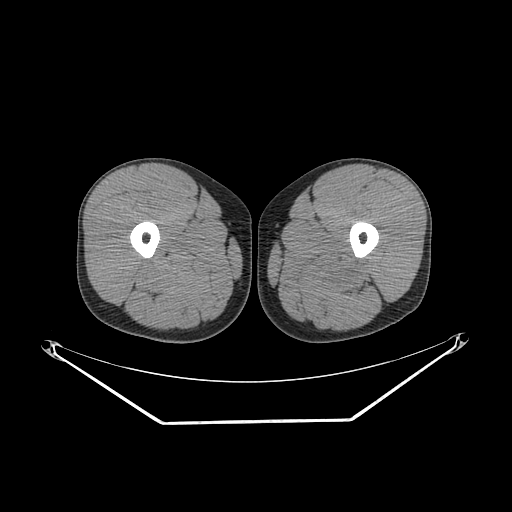
CT of an extremity soft-tissue mass (from a PET/CT study), one axial slice; slice 238 of 267 in the series (ordered by position); reconstruction kernel SOFT; 140 kVp; soft-tissue window (W 400 / L 40 HU); 3.75 mm slice thickness; 512 × 512 image matrix. Male patient. Case-level facts recorded for this patient, not image findings: histological type: extraskeletal osteosarcoma; grade: high; site of the primary tumour: left adductur.
Structures marked on this image (expert contour drawn on MRI and transferred to this co-registered scan by the dataset authors):
- gross tumour volume (mass): bounding box (x1, y1, x2, y2) in pixels: (279, 246, 380, 296)